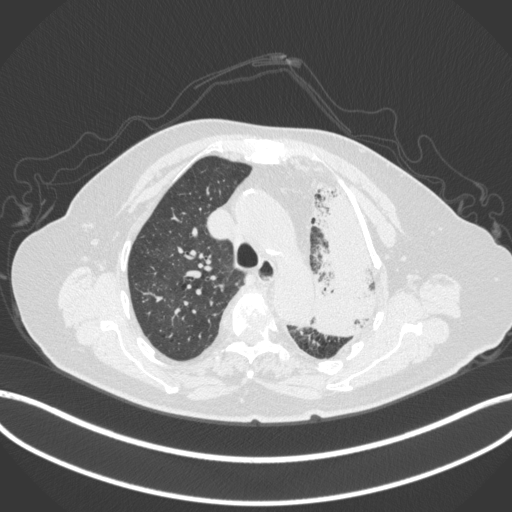
Chest CT, one axial slice; slice 289 of 399 in the series (ordered by position); lung window (W 1500 / L -600 HU); 512 × 512 image matrix, field of view 400 × 400 mm. Female patient, age 75 years. Case-level facts recorded for this patient, not image findings: clinical TNM (as recorded): T3 N3 M1.
Annotated regions visible in this slice (rectangle marked by the reading radiologist):
- lung tumour (recorded histology: adenocarcinoma): bounding box [x1, y1, x2, y2] px = [300, 182, 392, 343]